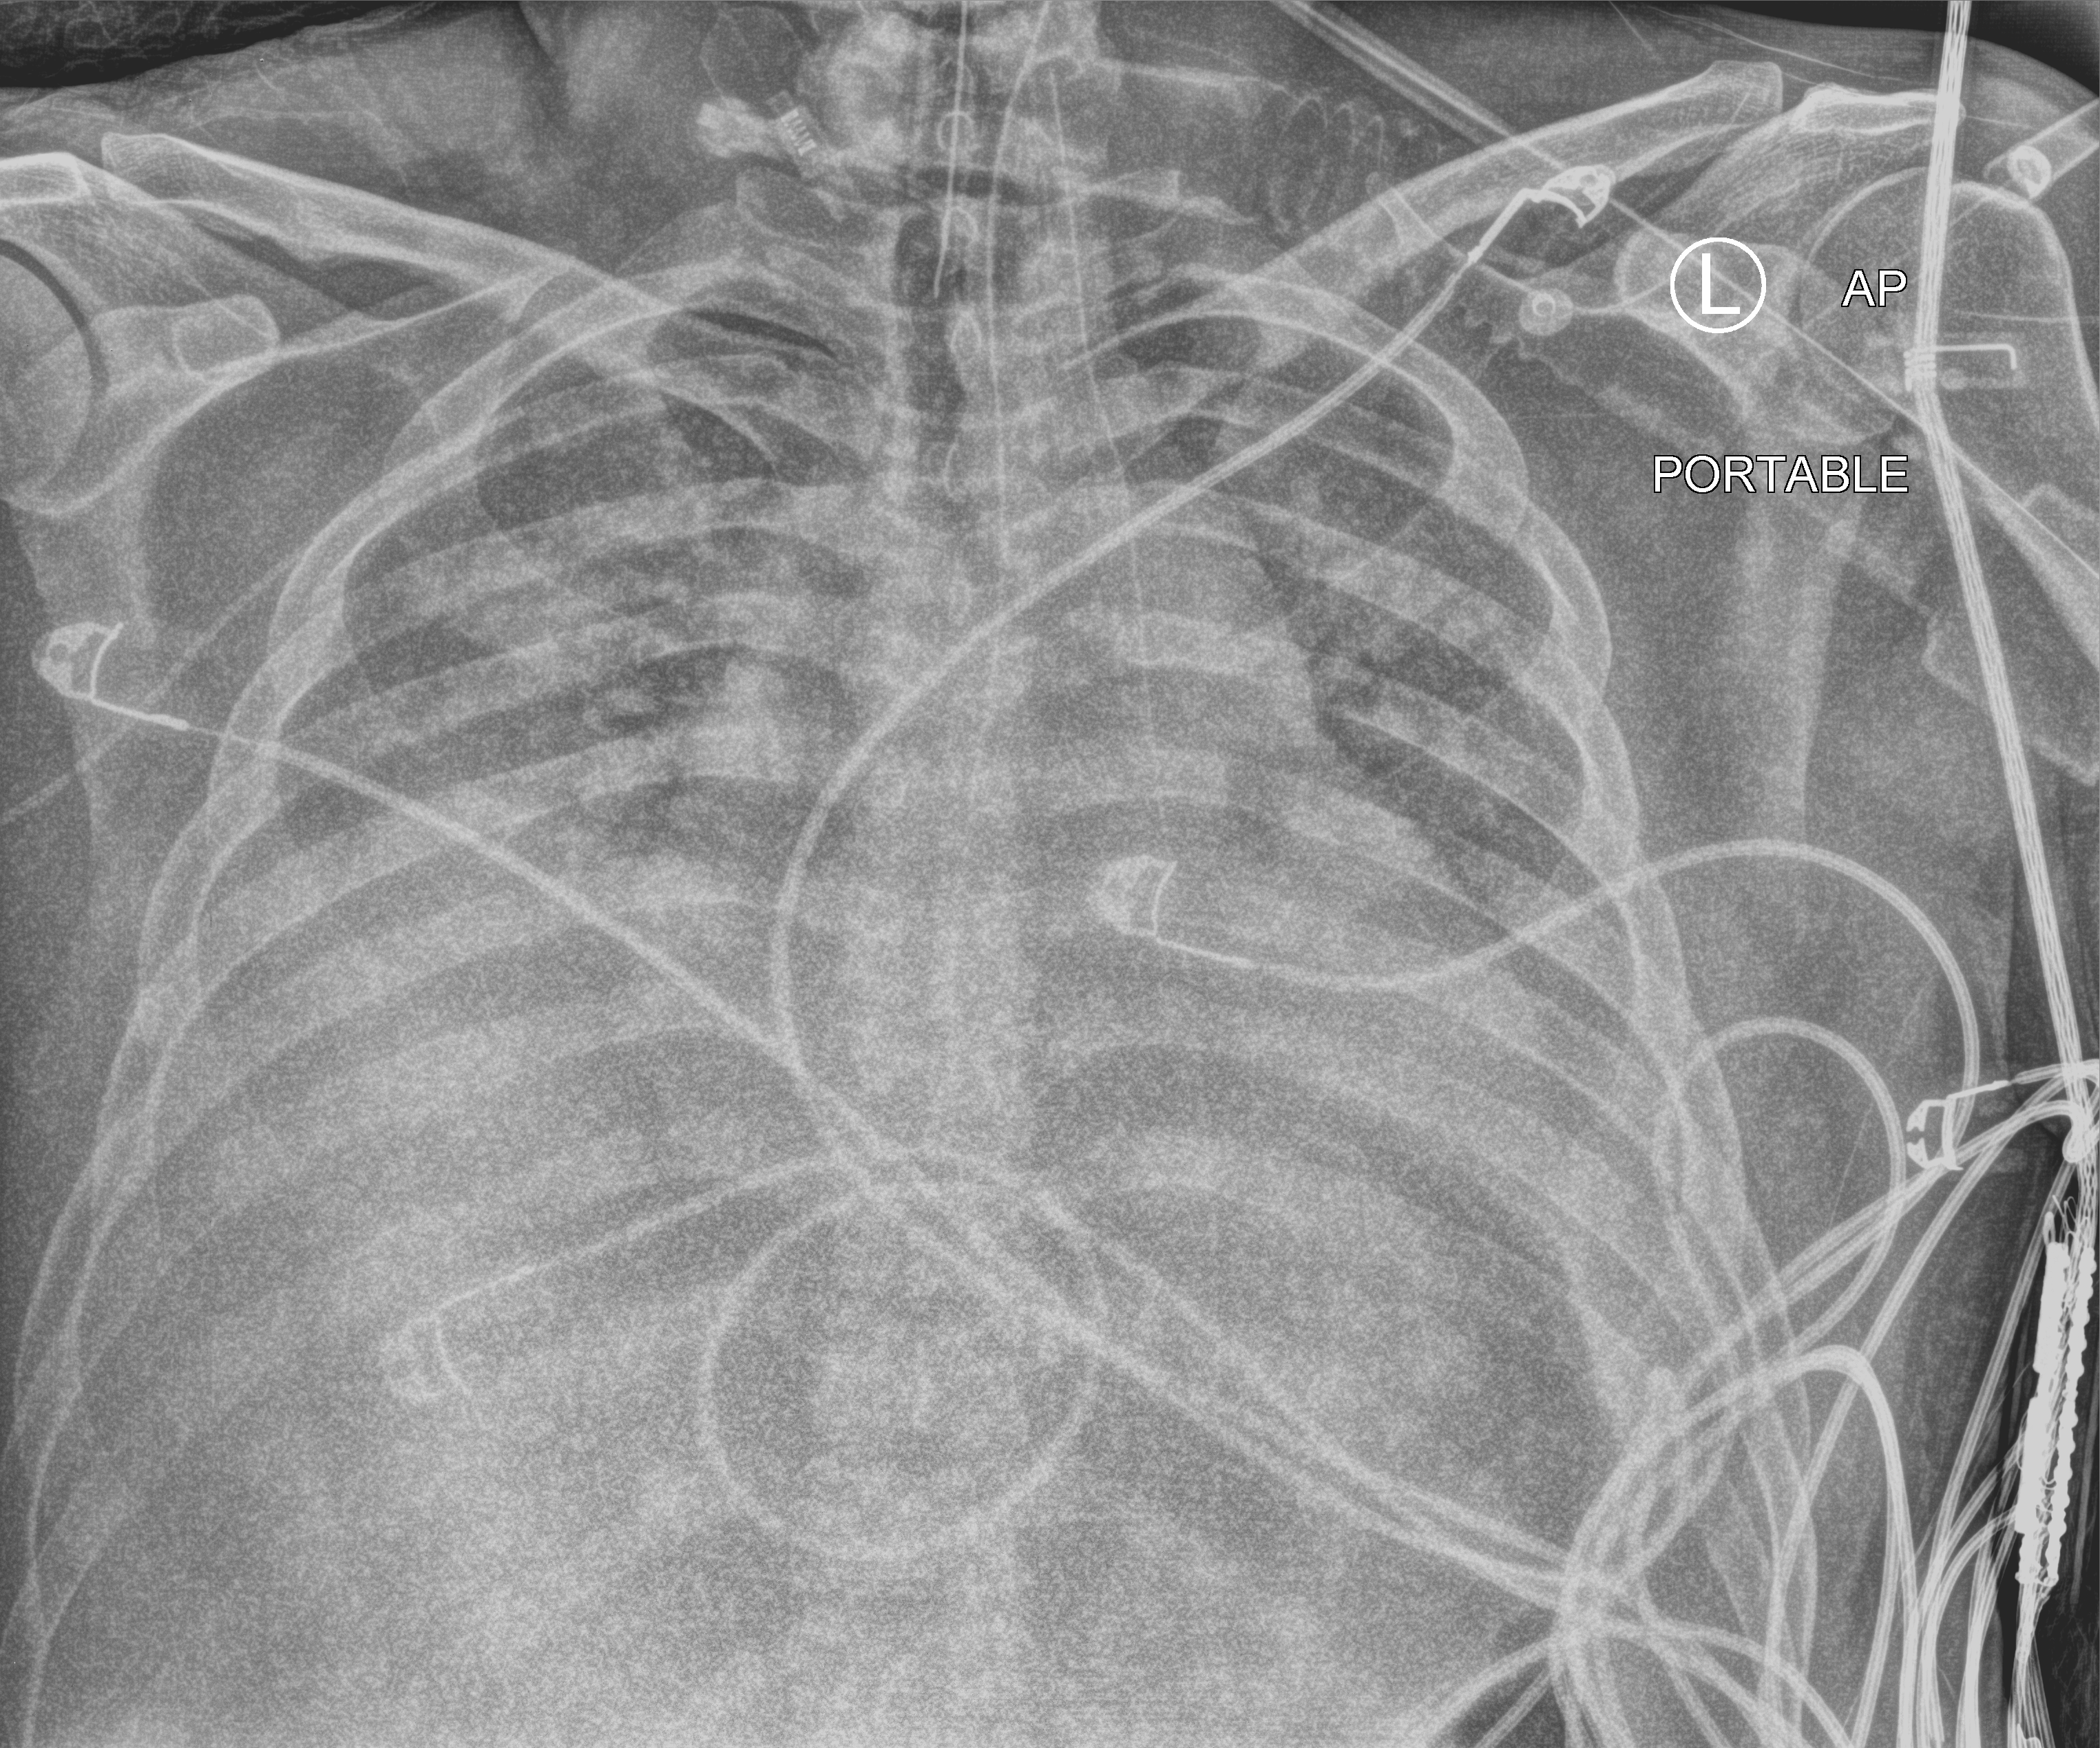
Chest X-ray (portable), anteroposterior (AP) projection. Male patient hospitalised with COVID-19, age 18–59 years.
Hospital-stay facts (about this admission, not read from this image; timing relative to this image not recorded):
- COPD (admission record): no
- smoking status (admission record): current
- mechanically ventilated during this hospital stay: yes